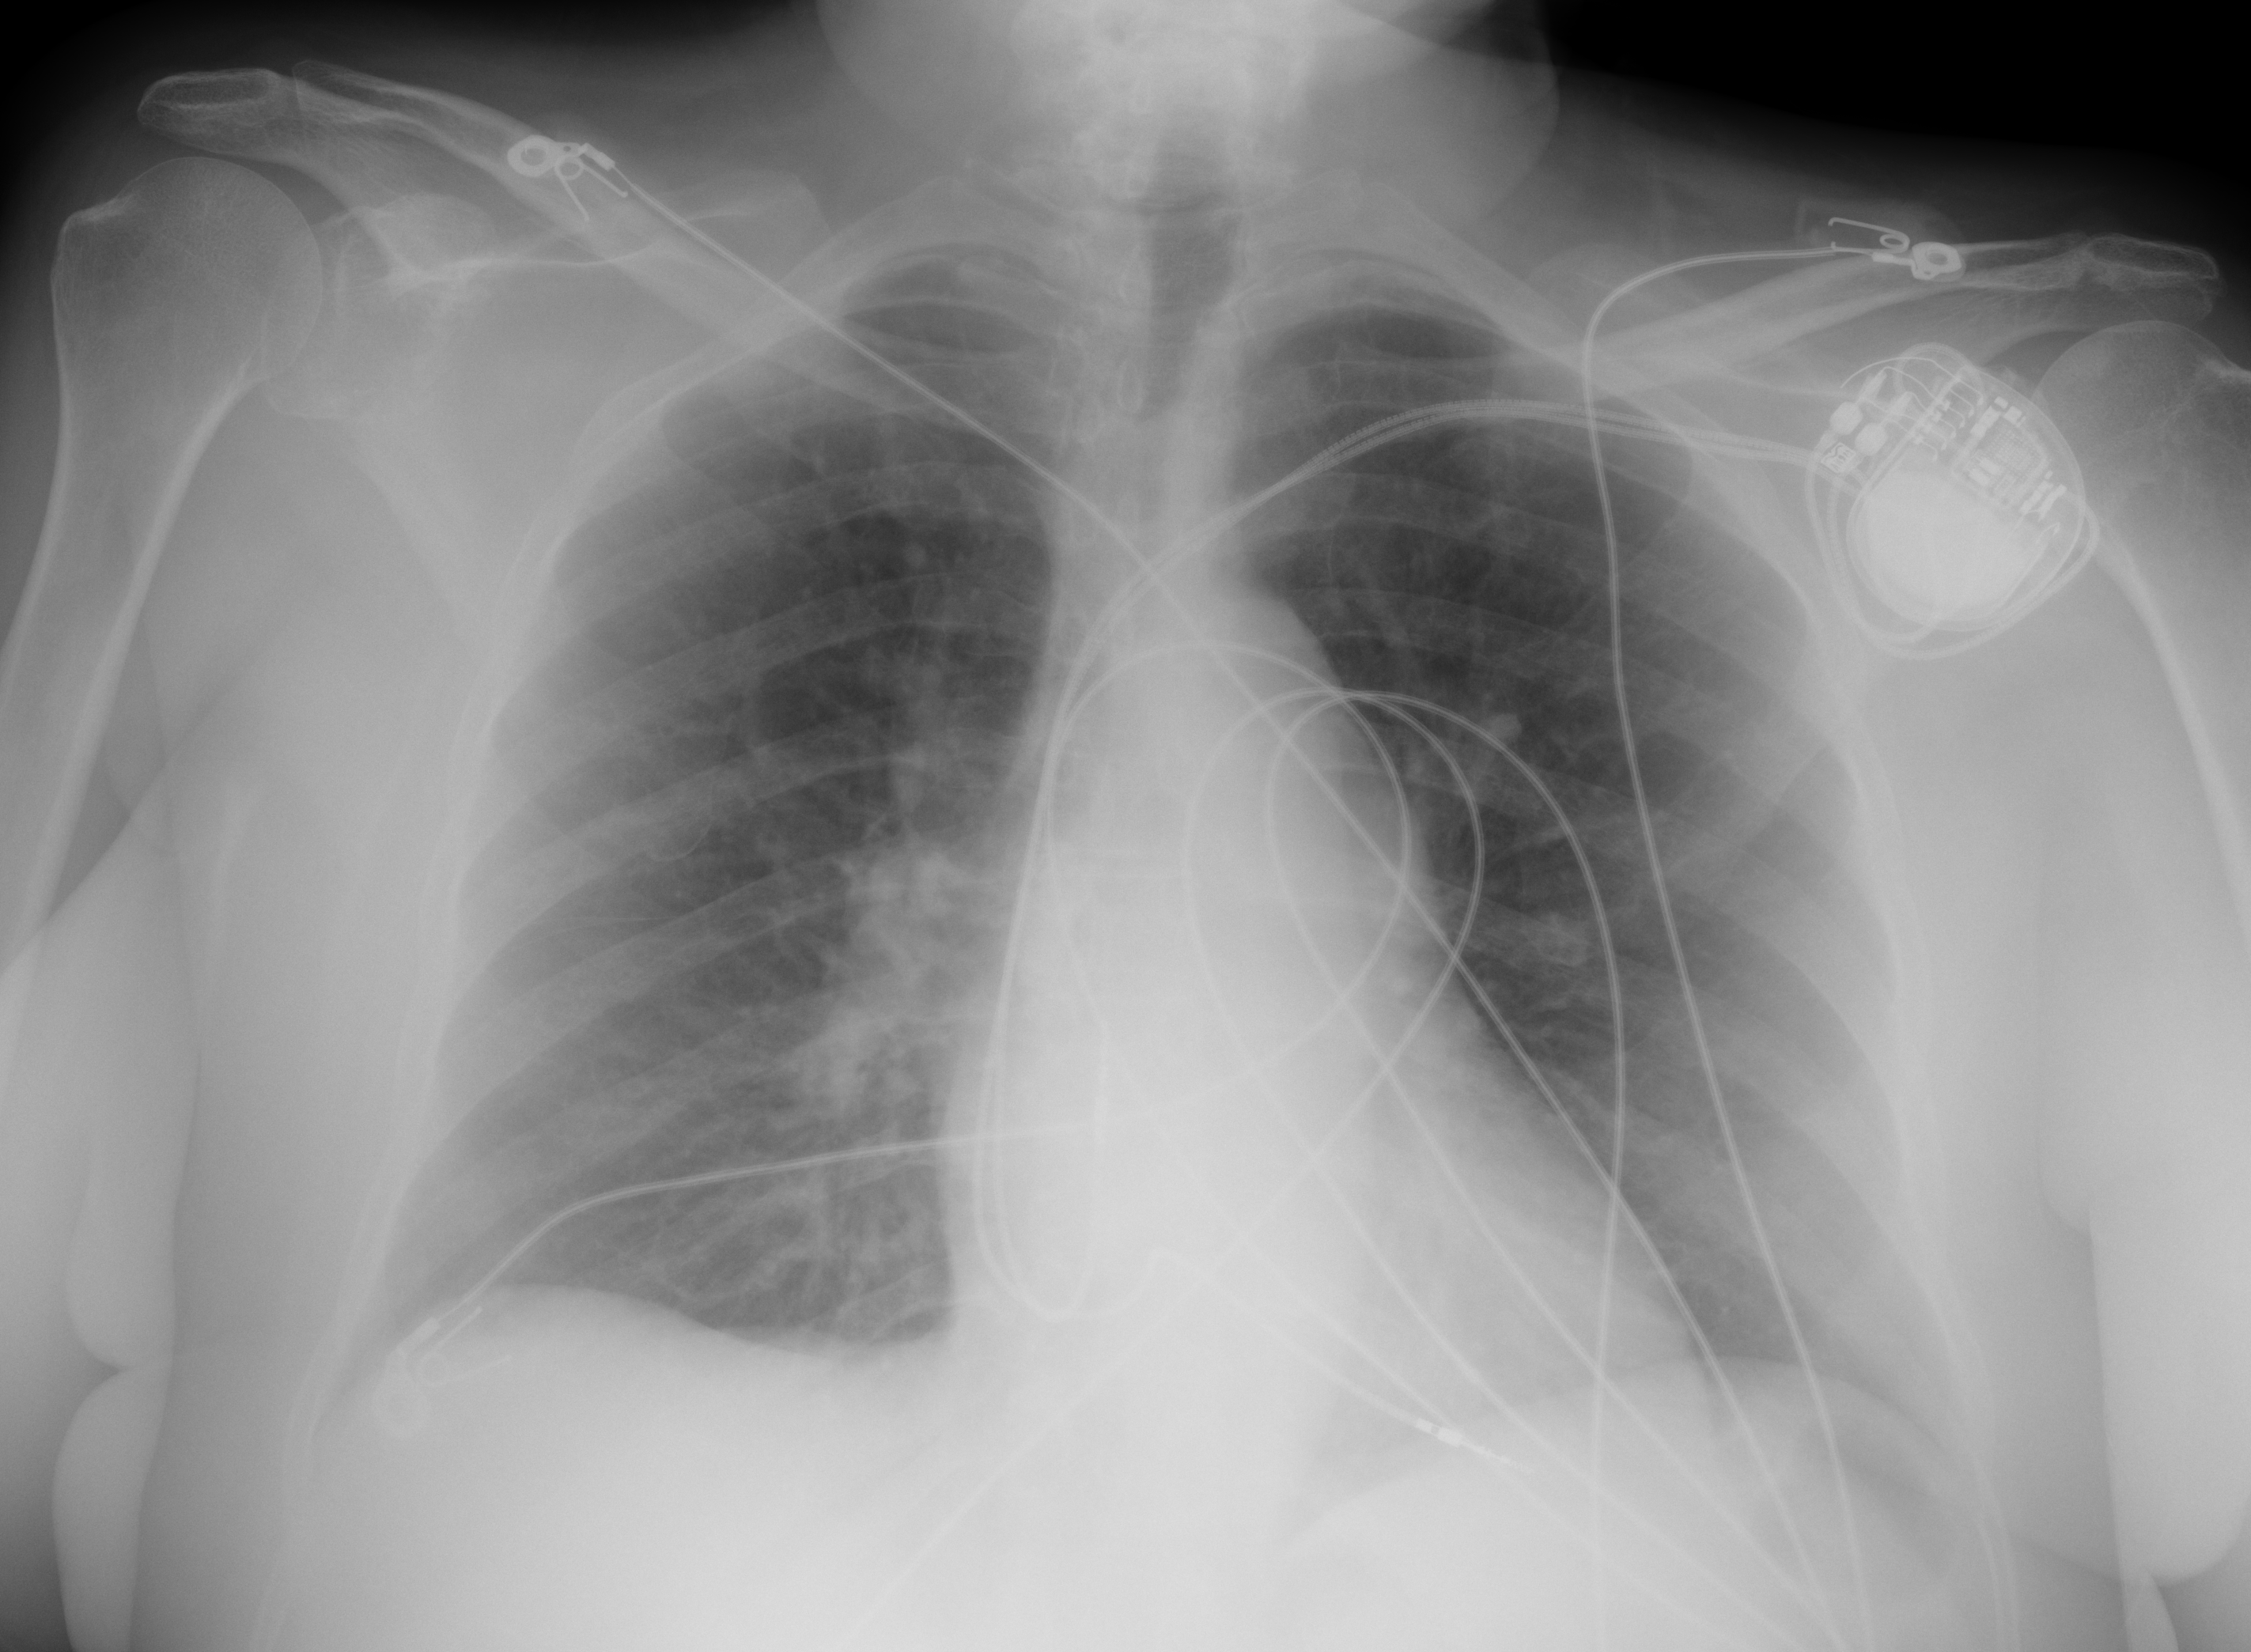
Portable chest radiograph, AP projection. Female patient, age 77 years; imaged 0 days after the COVID-19 diagnosis.
Radiologist's key findings for this exam: he lungs are well-aerated with no evidence of pneumonic infiltration or pleural effusion.